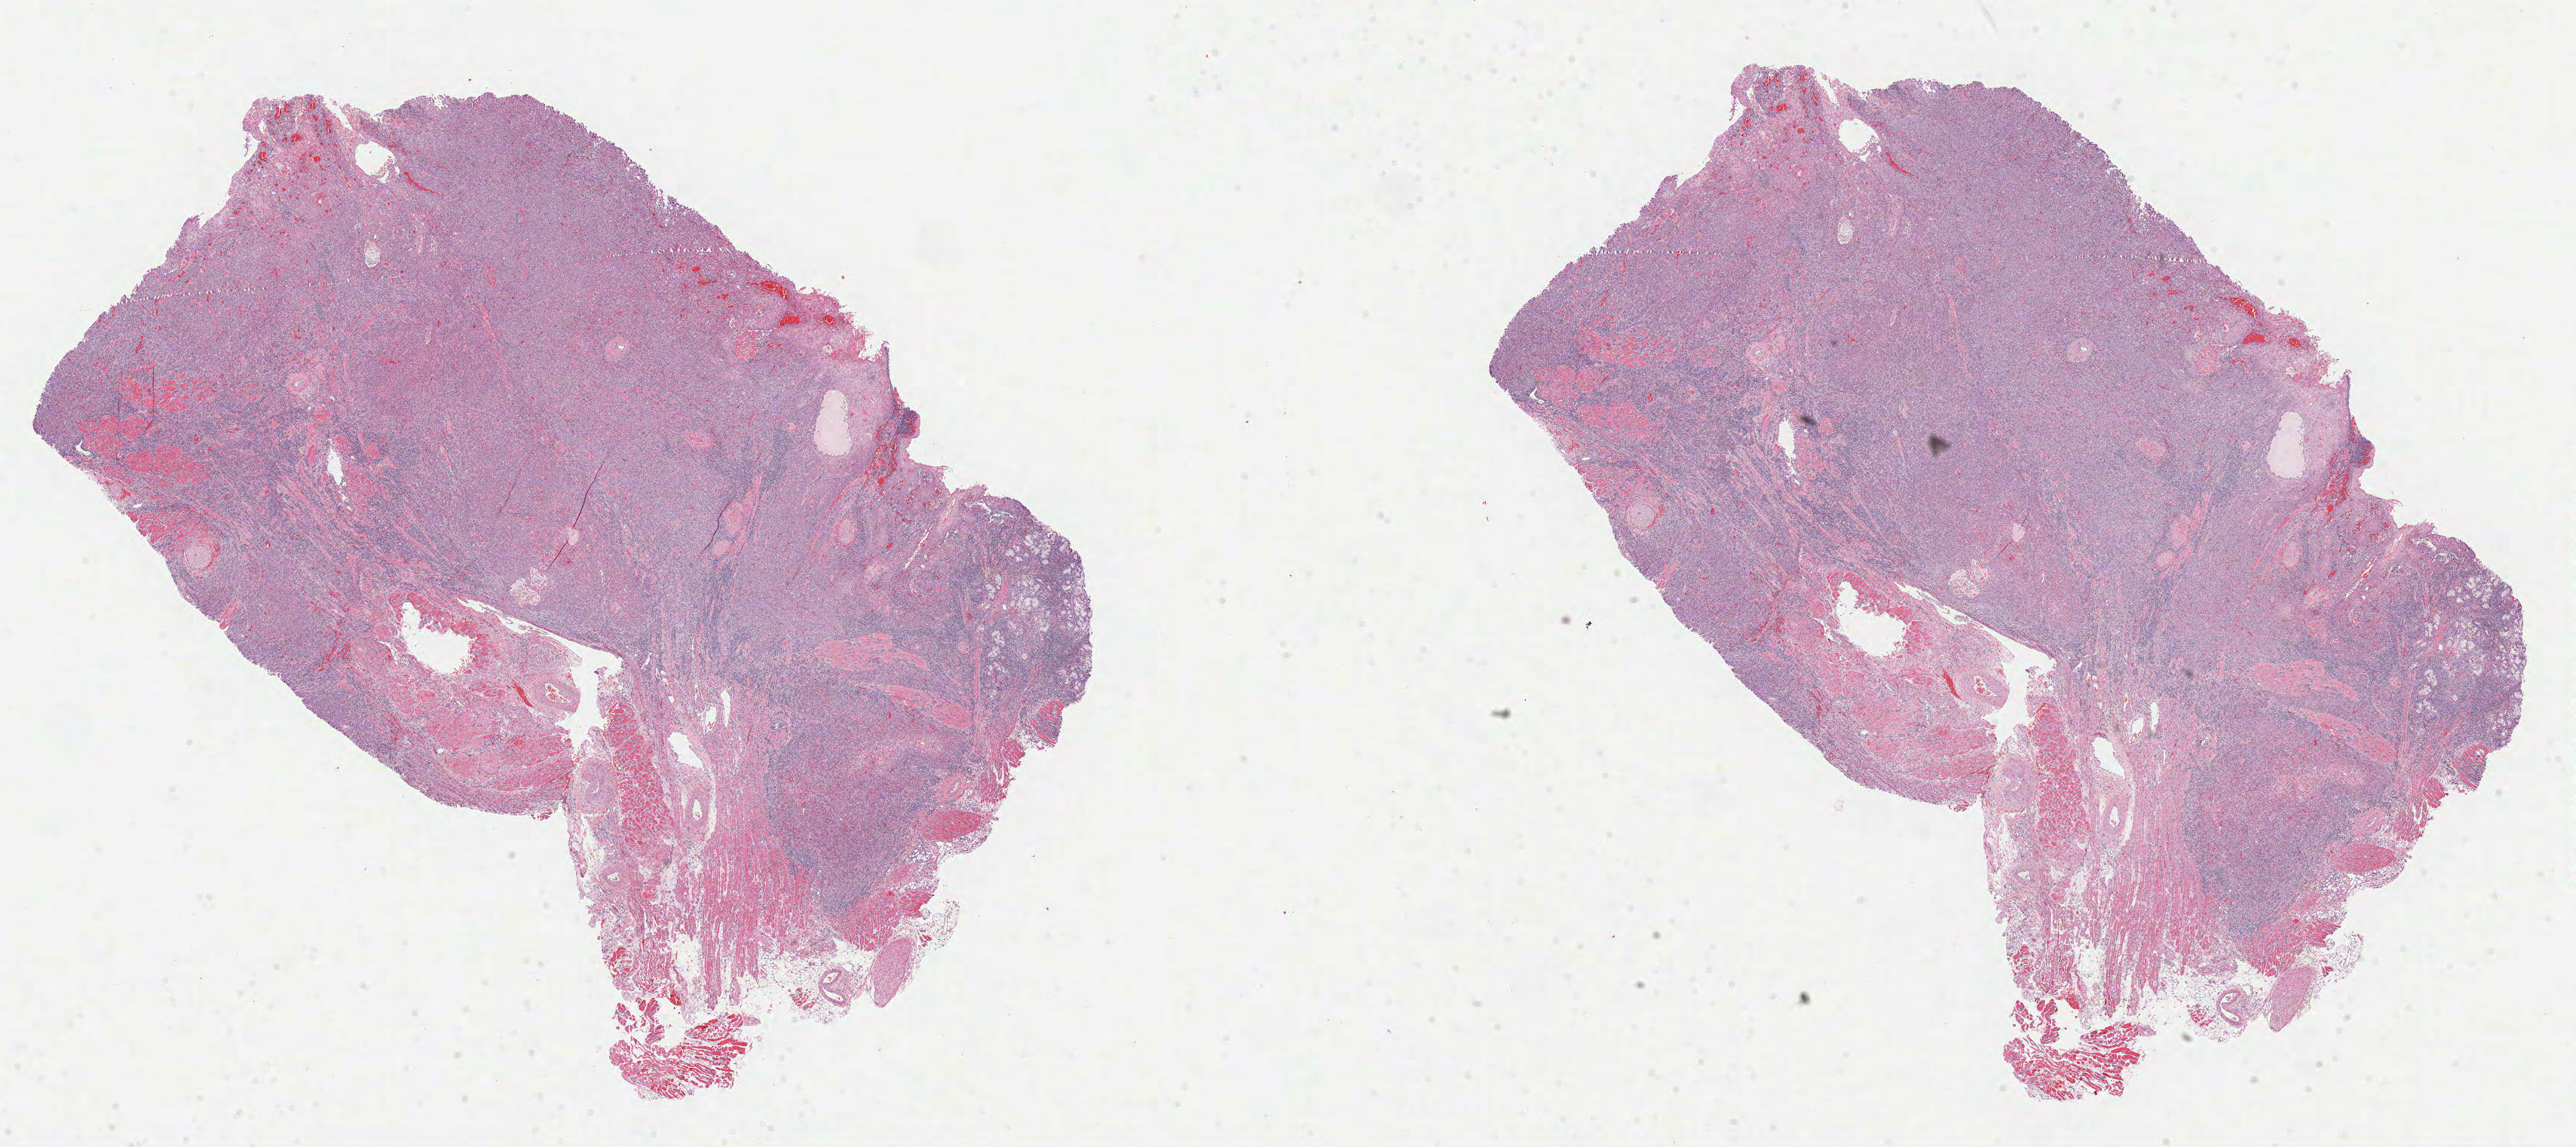
Whole-slide histology image, Hematoxylin and eosin (H&E) stained — a low-resolution overview of the entire scanned area, about 27.6 x 12.3 mm (acquisition: 40x scan); FFPE section; sample: primary tumour, head and neck. Patient: male, age at initial diagnosis 55 years.
Histologic diagnosis: Squamous cell carcinoma, NOS.